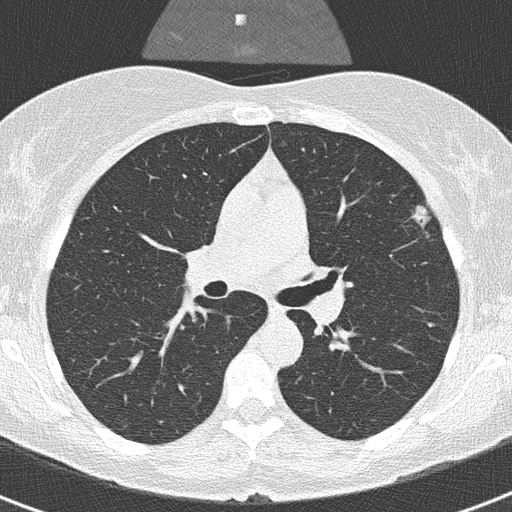
Low-dose screening chest CT, one axial slice. Slice 203 of 320 in the series (ordered by position). Reconstruction kernel B50f. 120 kVp. Lung window (W 1500 / L -600 HU). 2 mm slice thickness. 512 × 512 image matrix.
Outlined on this slice (manually delineated by an expert):
- lesion 1 (tumor, upper lobe of left lung): bounding box <413,205,430,226> (left, top, right, bottom; pixels)